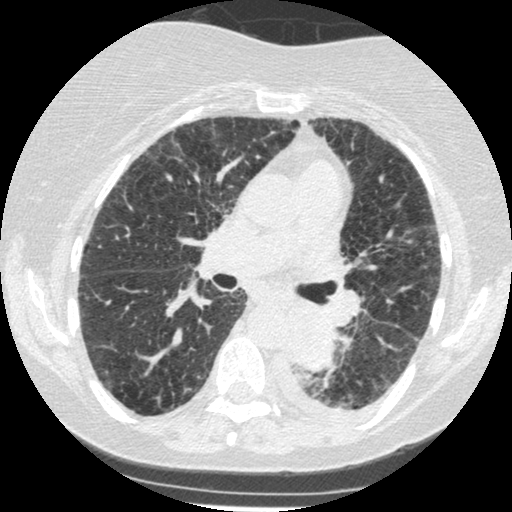
Low-dose screening chest CT, one axial slice. Position 144 of 341 along the scan axis. Lung window (W 1500 / L -600 HU). 1.25 mm slice thickness. 512 × 512 image matrix, field of view 310 × 310 mm.
Annotated regions visible in this slice (expert manual segmentation):
- lesion 1 (tumor, lower lobe of left lung): bounding box [x1, y1, x2, y2] px = [285, 306, 336, 371]